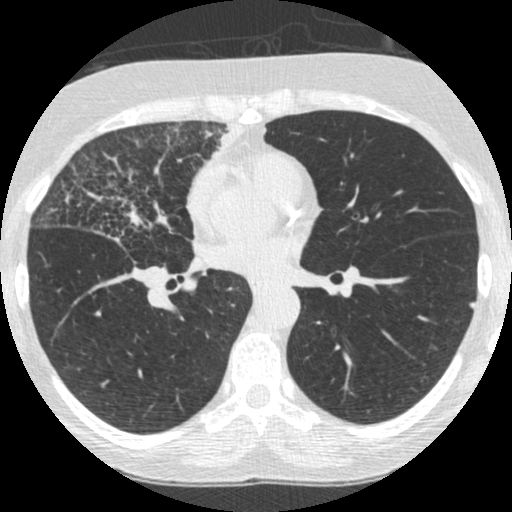
Low-dose screening chest CT, one axial slice; position 130 of 253 along the scan axis; reconstruction kernel STANDARD; lung window (W 1500 / L -600 HU); 512 × 512 image matrix.
Annotated regions visible in this slice (manually delineated by an expert):
- lesion 4 (tumor, upper lobe of right lung): bounding box [x1, y1, x2, y2] px = [209, 121, 243, 158]